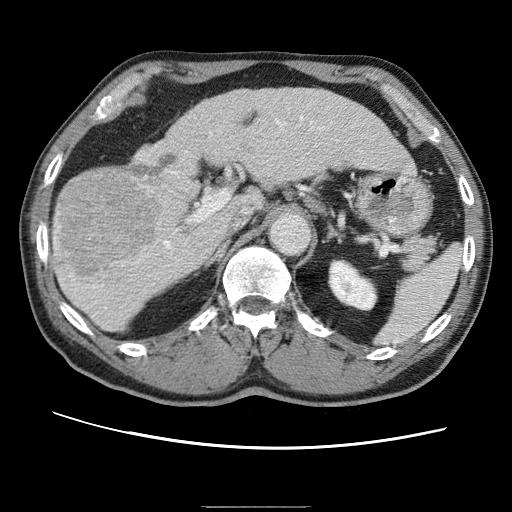
Contrast-enhanced abdominal CT (liver protocol), one axial slice. Slice 31 of 75 in the series (ordered by position). Reconstruction kernel STANDARD. 120 kVp. One of 2 acquisitions stored at this slice position. Soft-tissue window (W 400 / L 40 HU). 2.5 mm slice thickness. 512 × 512 image matrix, field of view 360 × 360 mm. Case-level facts recorded for this patient, not image findings: diagnosis: hepatocellular carcinoma (patient treated with transarterial chemoembolisation; whether this scan precedes or follows treatment is not stated here); TNM stage (as recorded): Stage-II; Child-Pugh class: A; tumour differentiation: well differentiated; tumour nodularity: multinodular.
Outlined on this slice (semi-automatic segmentation, software-assisted and operator-edited):
- liver parenchyma outside the tumour (the mass and vessels are separate outlines, so this box may not span the whole liver): box from (x=54, y=88) to (x=408, y=330) px
- mass: (x=54, y=169)–(x=159, y=281)
- liver vessels: (x=85, y=104)–(x=346, y=299)